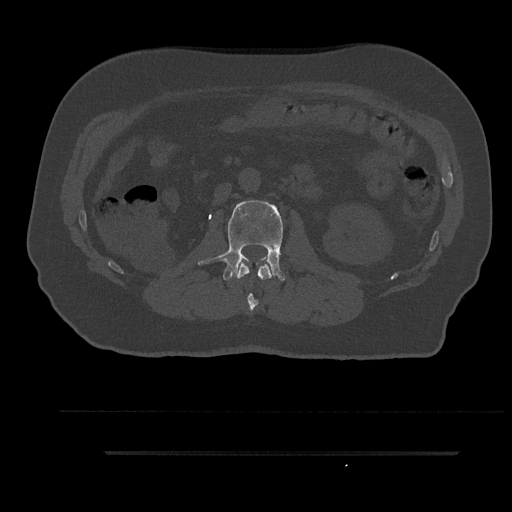
CT including the spine, one axial slice. Slice 127 of 797 in the series (ordered by position). Bone window (W 1800 / L 400 HU). 0.5 mm slice thickness. 512 × 512 image matrix, field of view 432 × 432 mm. Patient: male, 63 years. Case-level facts recorded for this patient, not image findings: primary cancer: renal.
Annotated regions visible in this slice (semi-automatically segmented with operator editing):
- L1 vertebra: box from (x=236, y=261) to (x=275, y=312) px
- L2 vertebra: (x=198, y=200)–(x=285, y=281)